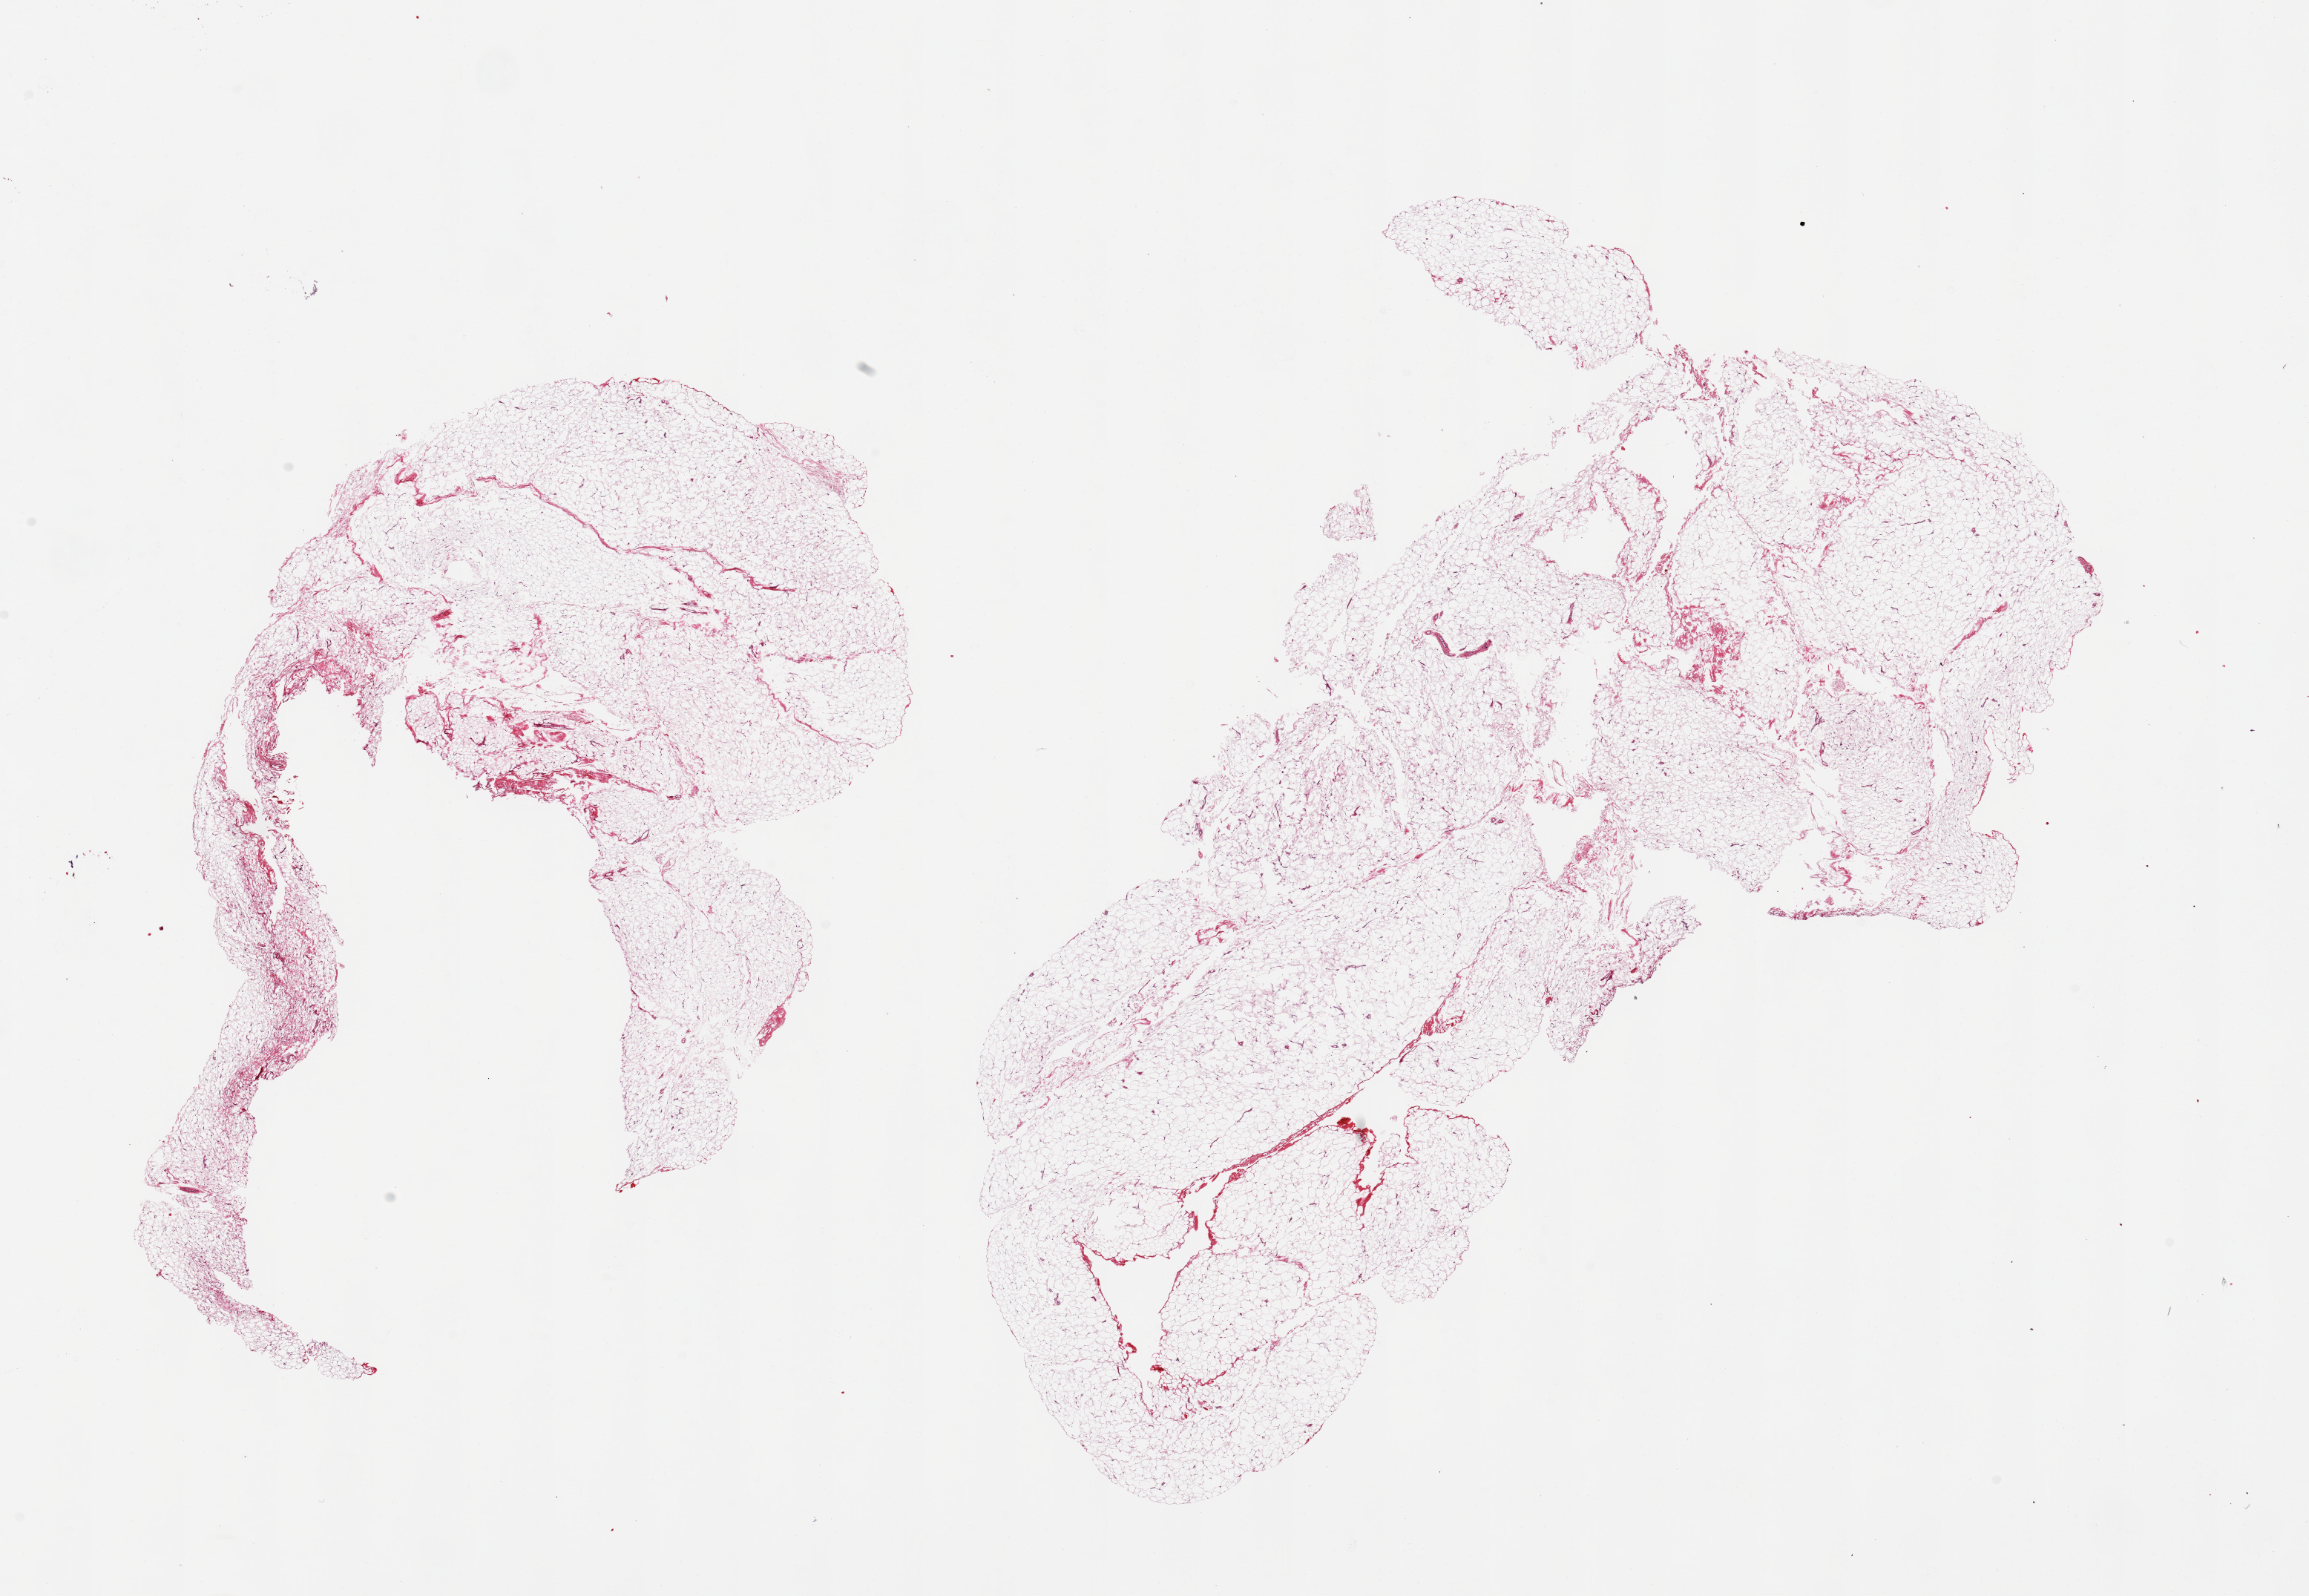
Digitized haematoxylin and eosin-stained section — shown as a low-resolution overview of the whole scanned area (about 24.6 x 17.0 mm), PAXgene-fixed paraffin-embedded (PFPE) section, target tissue: adipose tissue, donor tissue sample. Donor sex: female.
Review note (as recorded): 2 pieces; <5% fibrous content.